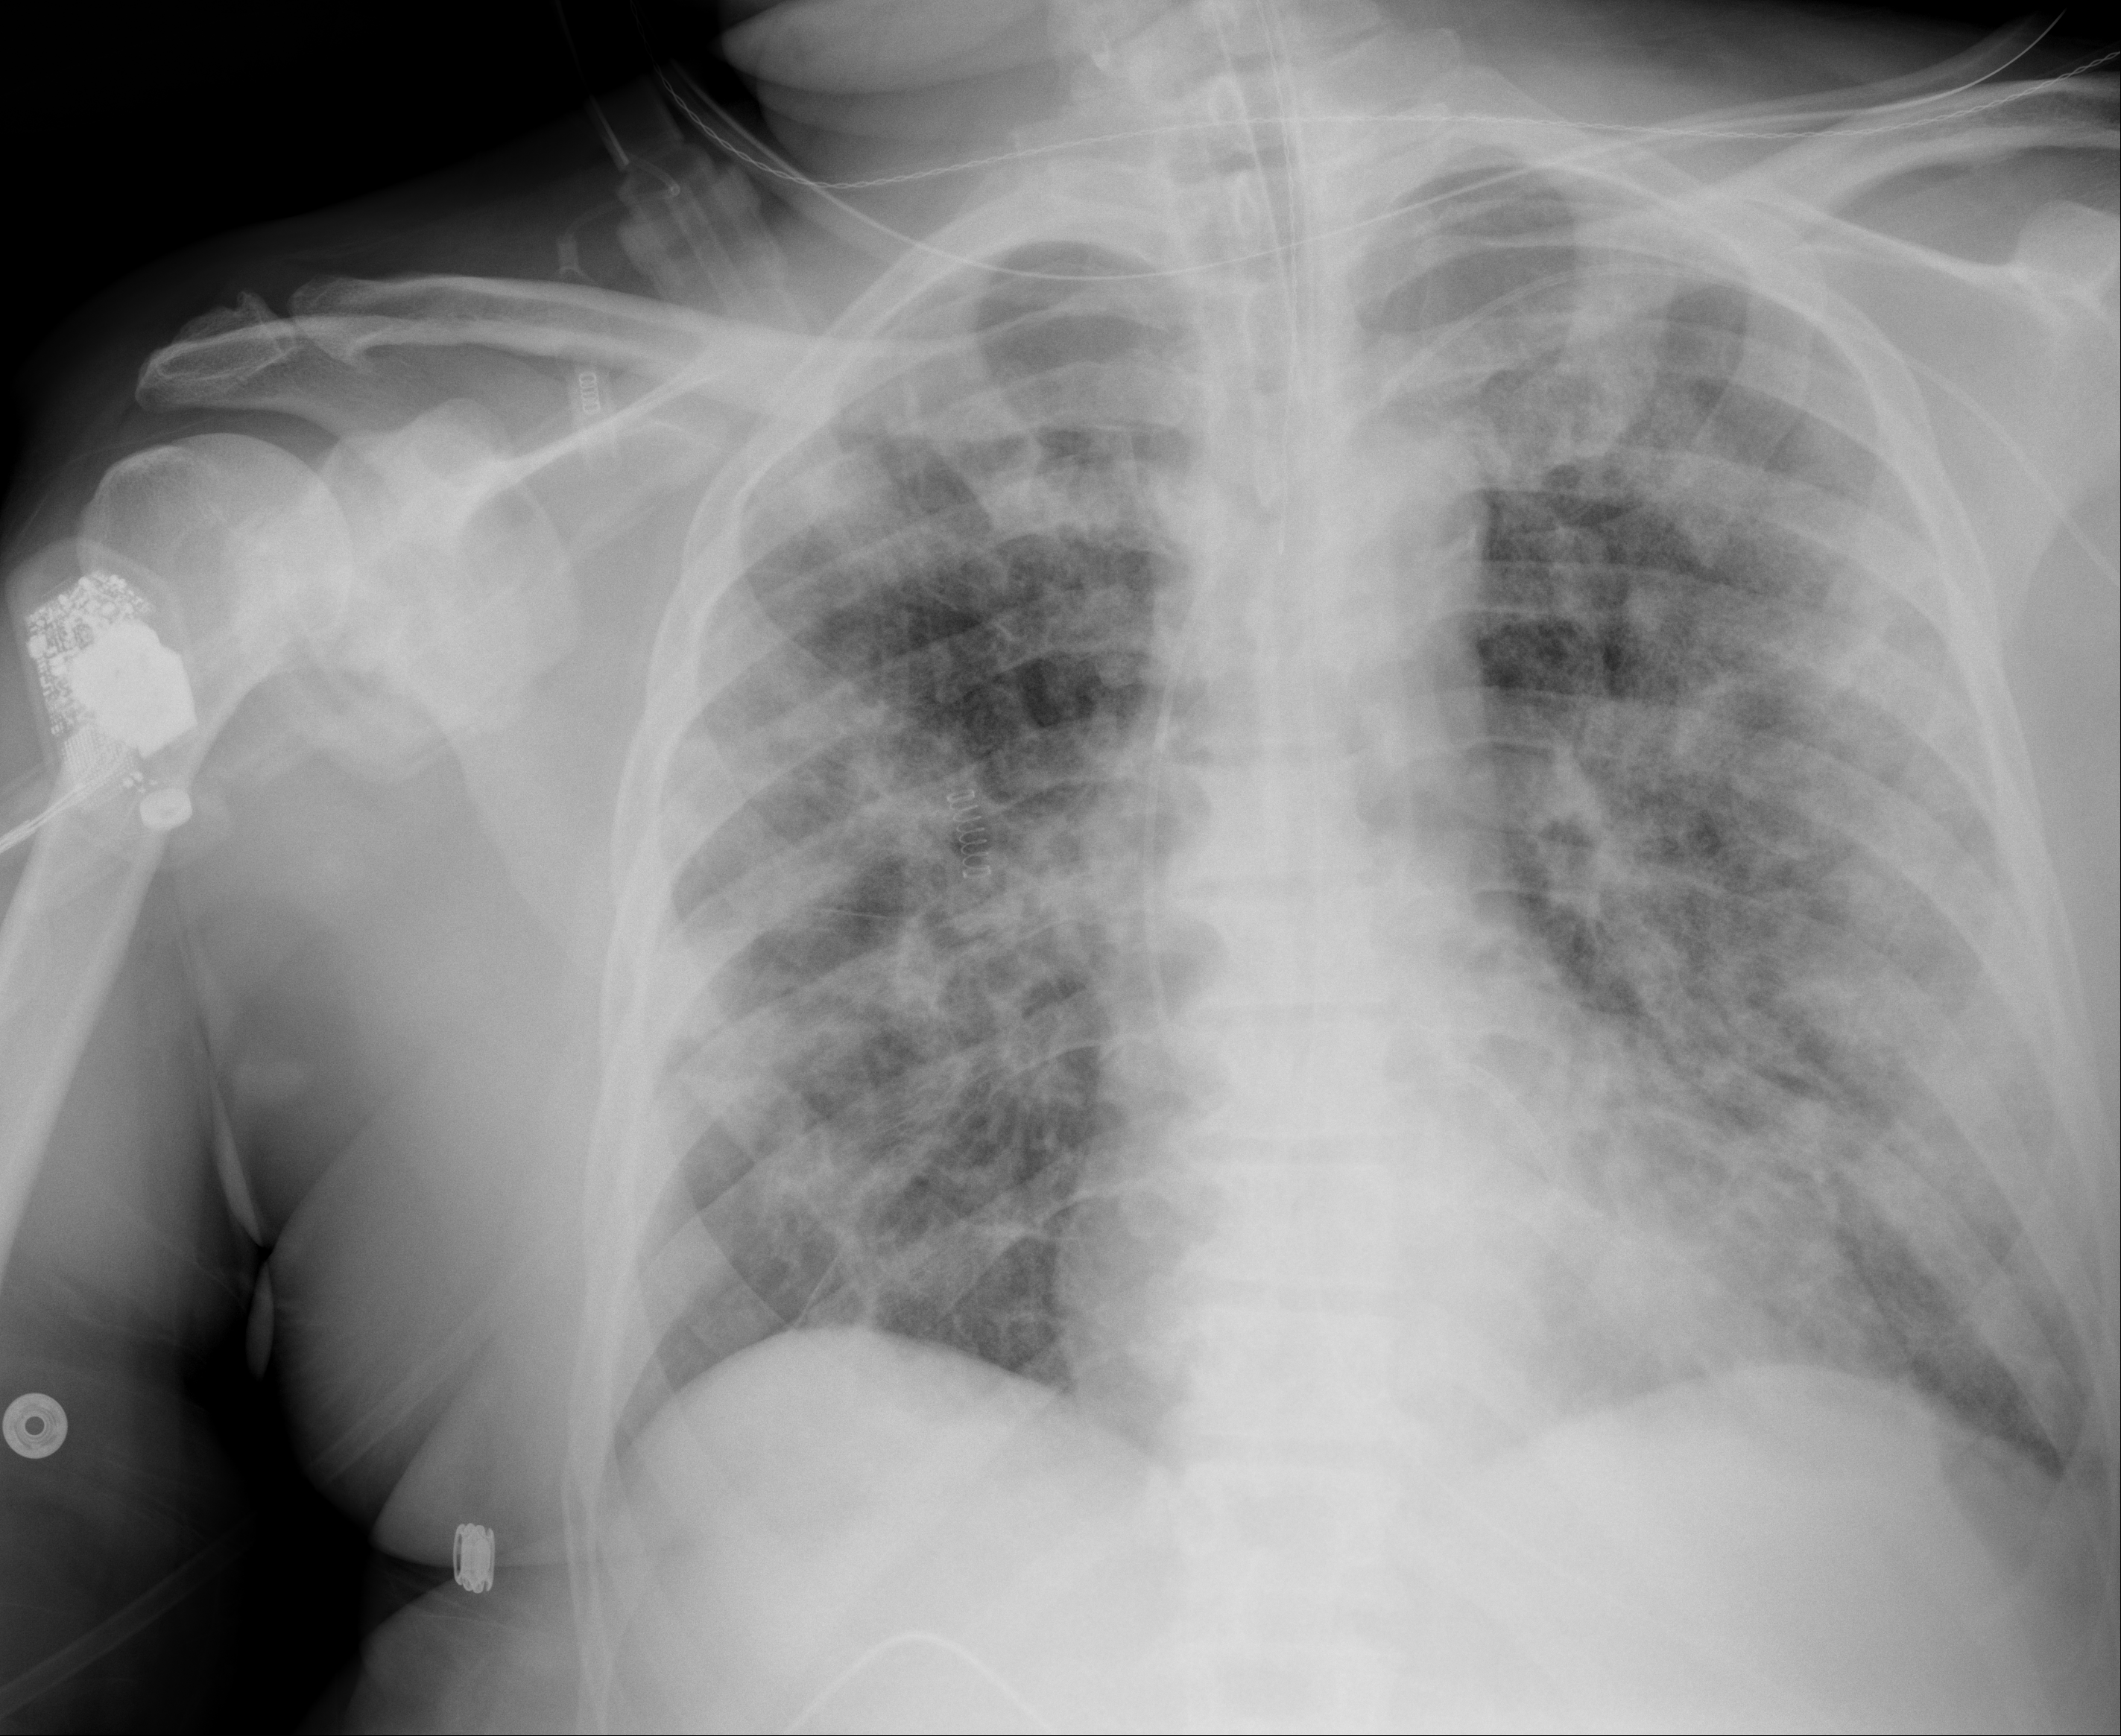
Chest X-ray (portable), AP projection. Male patient, age 64 years; imaged 6 days after the COVID-19 diagnosis.
Radiologist key findings (as recorded): Patchy airspace opacities throughout both lungs, without significant change.